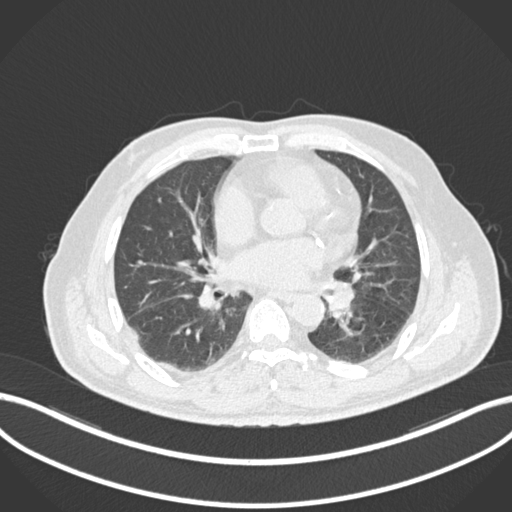
Chest CT, one axial slice; position 64 of 161 along the scan axis; reconstruction kernel B30f; lung window (W 1500 / L -600 HU); 1 mm slice thickness; 512 × 512 image matrix, field of view 400 × 400 mm. Male patient, age 71 years. Case-level facts recorded for this patient, not image findings: clinical TNM (as recorded): T1b N0 M0.
Outlined on this slice (rectangle marked by the reading radiologist):
- lung tumour (recorded histology: squamous cell carcinoma): bounding box <328,279,353,313> (left, top, right, bottom; pixels)